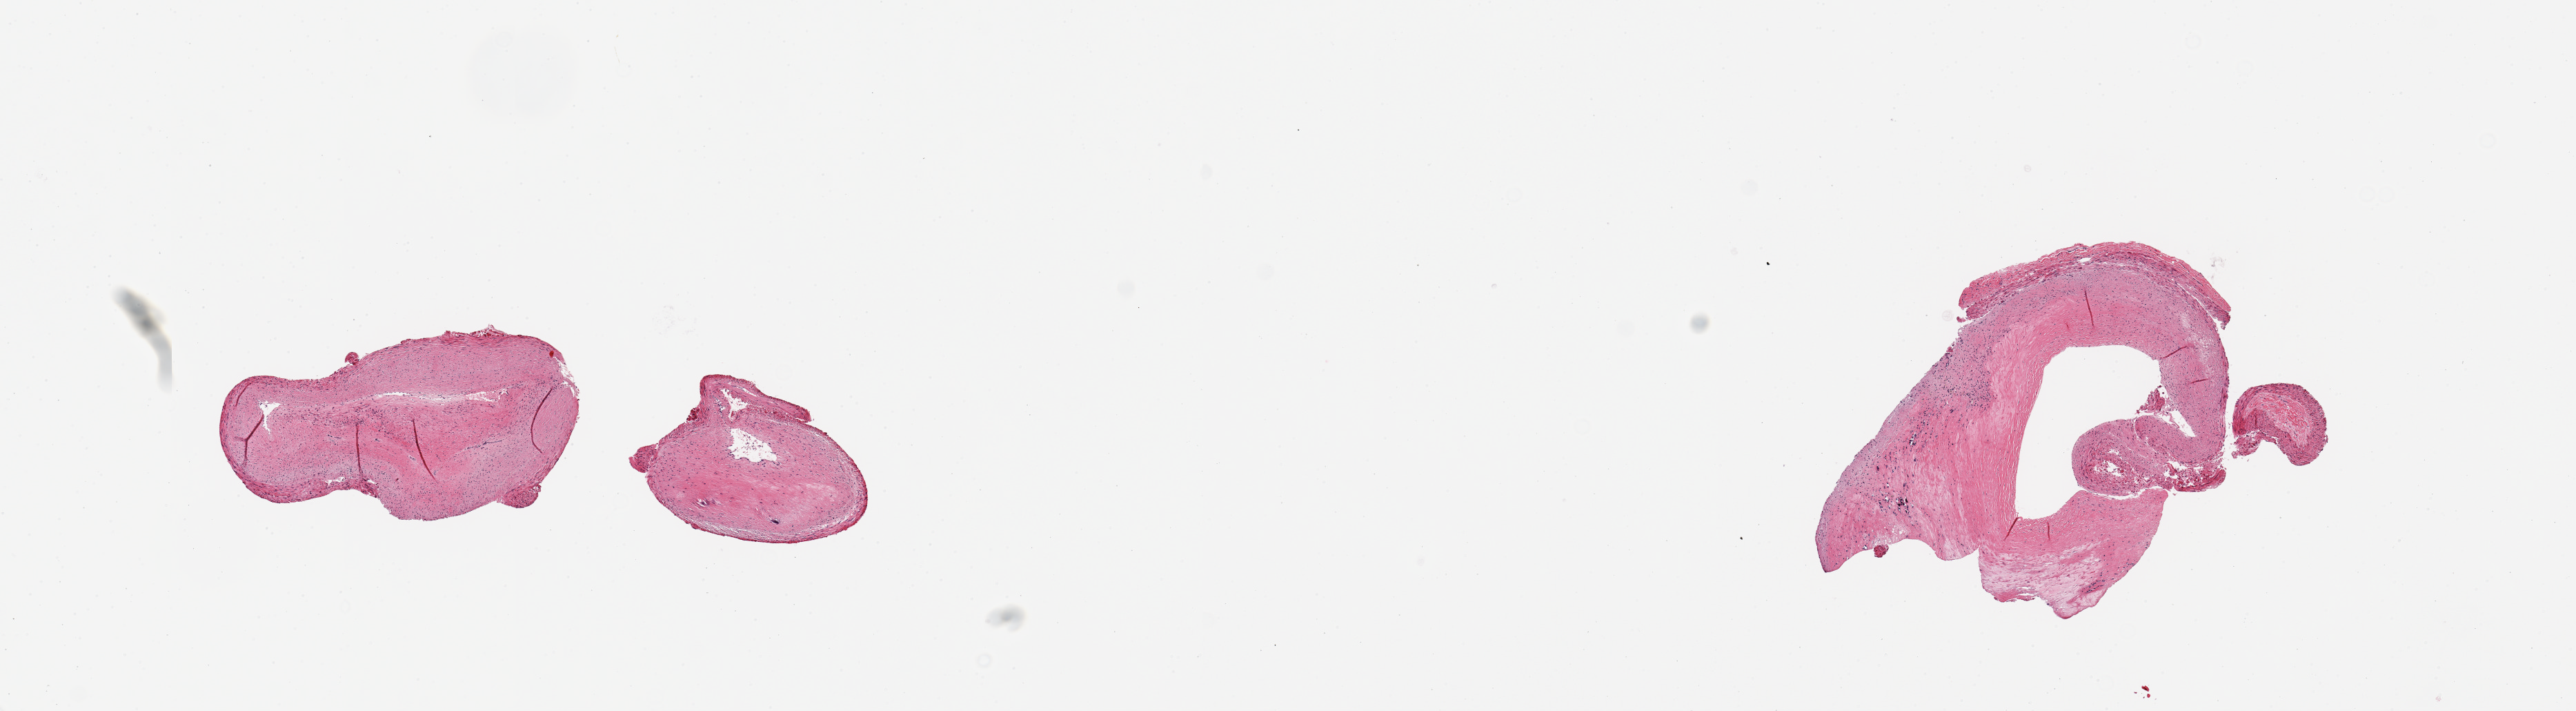
Haematoxylin and eosin whole-slide image — shown as a low-resolution overview of the whole scanned area (about 14.8 x 4.1 mm, slide scanned at 20x), PAXgene-fixed paraffin-embedded (PFPE) section, section of coronary artery (target tissue), tissue donor sample. Male donor.
Pathologist's review note for this sample: 2 pieces, subtotally occlusive atherosis.